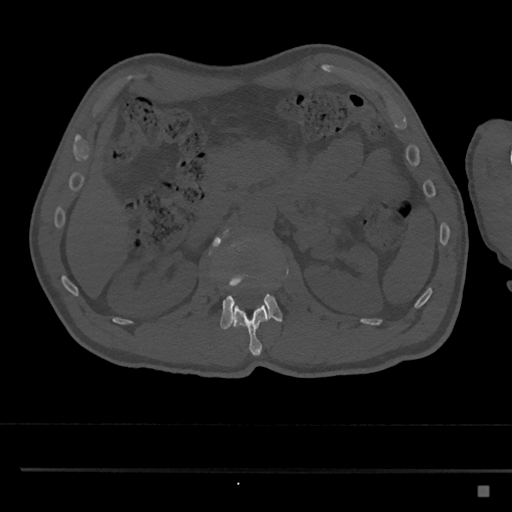
CT including the spine, one axial slice; bone window (W 1800 / L 400 HU); 0.5 mm slice thickness; 512 × 512 image matrix, field of view 391 × 391 mm. Patient: male, 59 years. From the clinical record (not read from this slice): primary cancer: prostate.
Outlined on this slice (semi-automatically segmented with operator editing):
- L1 vertebra: bounding box (x1, y1, x2, y2) in pixels: (233, 301, 269, 356)
- L2 vertebra: (209, 229, 282, 330)